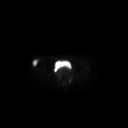
FDG PET of an extremity soft-tissue mass (from a PET/CT study), one axial slice. Slice 69 of 267 in the series (ordered by position). 128 × 128 image matrix, field of view 700 × 700 mm. Female patient, age 34 years. From the clinical record (not read from this slice): histological type: synovial sarcoma; grade: intermediate; site of the primary tumour: right thigh.
Structures marked on this image (expert contour drawn on MRI and transferred to this co-registered scan by the dataset authors):
- gross tumour volume including surrounding oedema: bounding box (x1, y1, x2, y2) in pixels: (31, 58, 39, 67)
- gross tumour volume (mass): (31, 59, 38, 67)